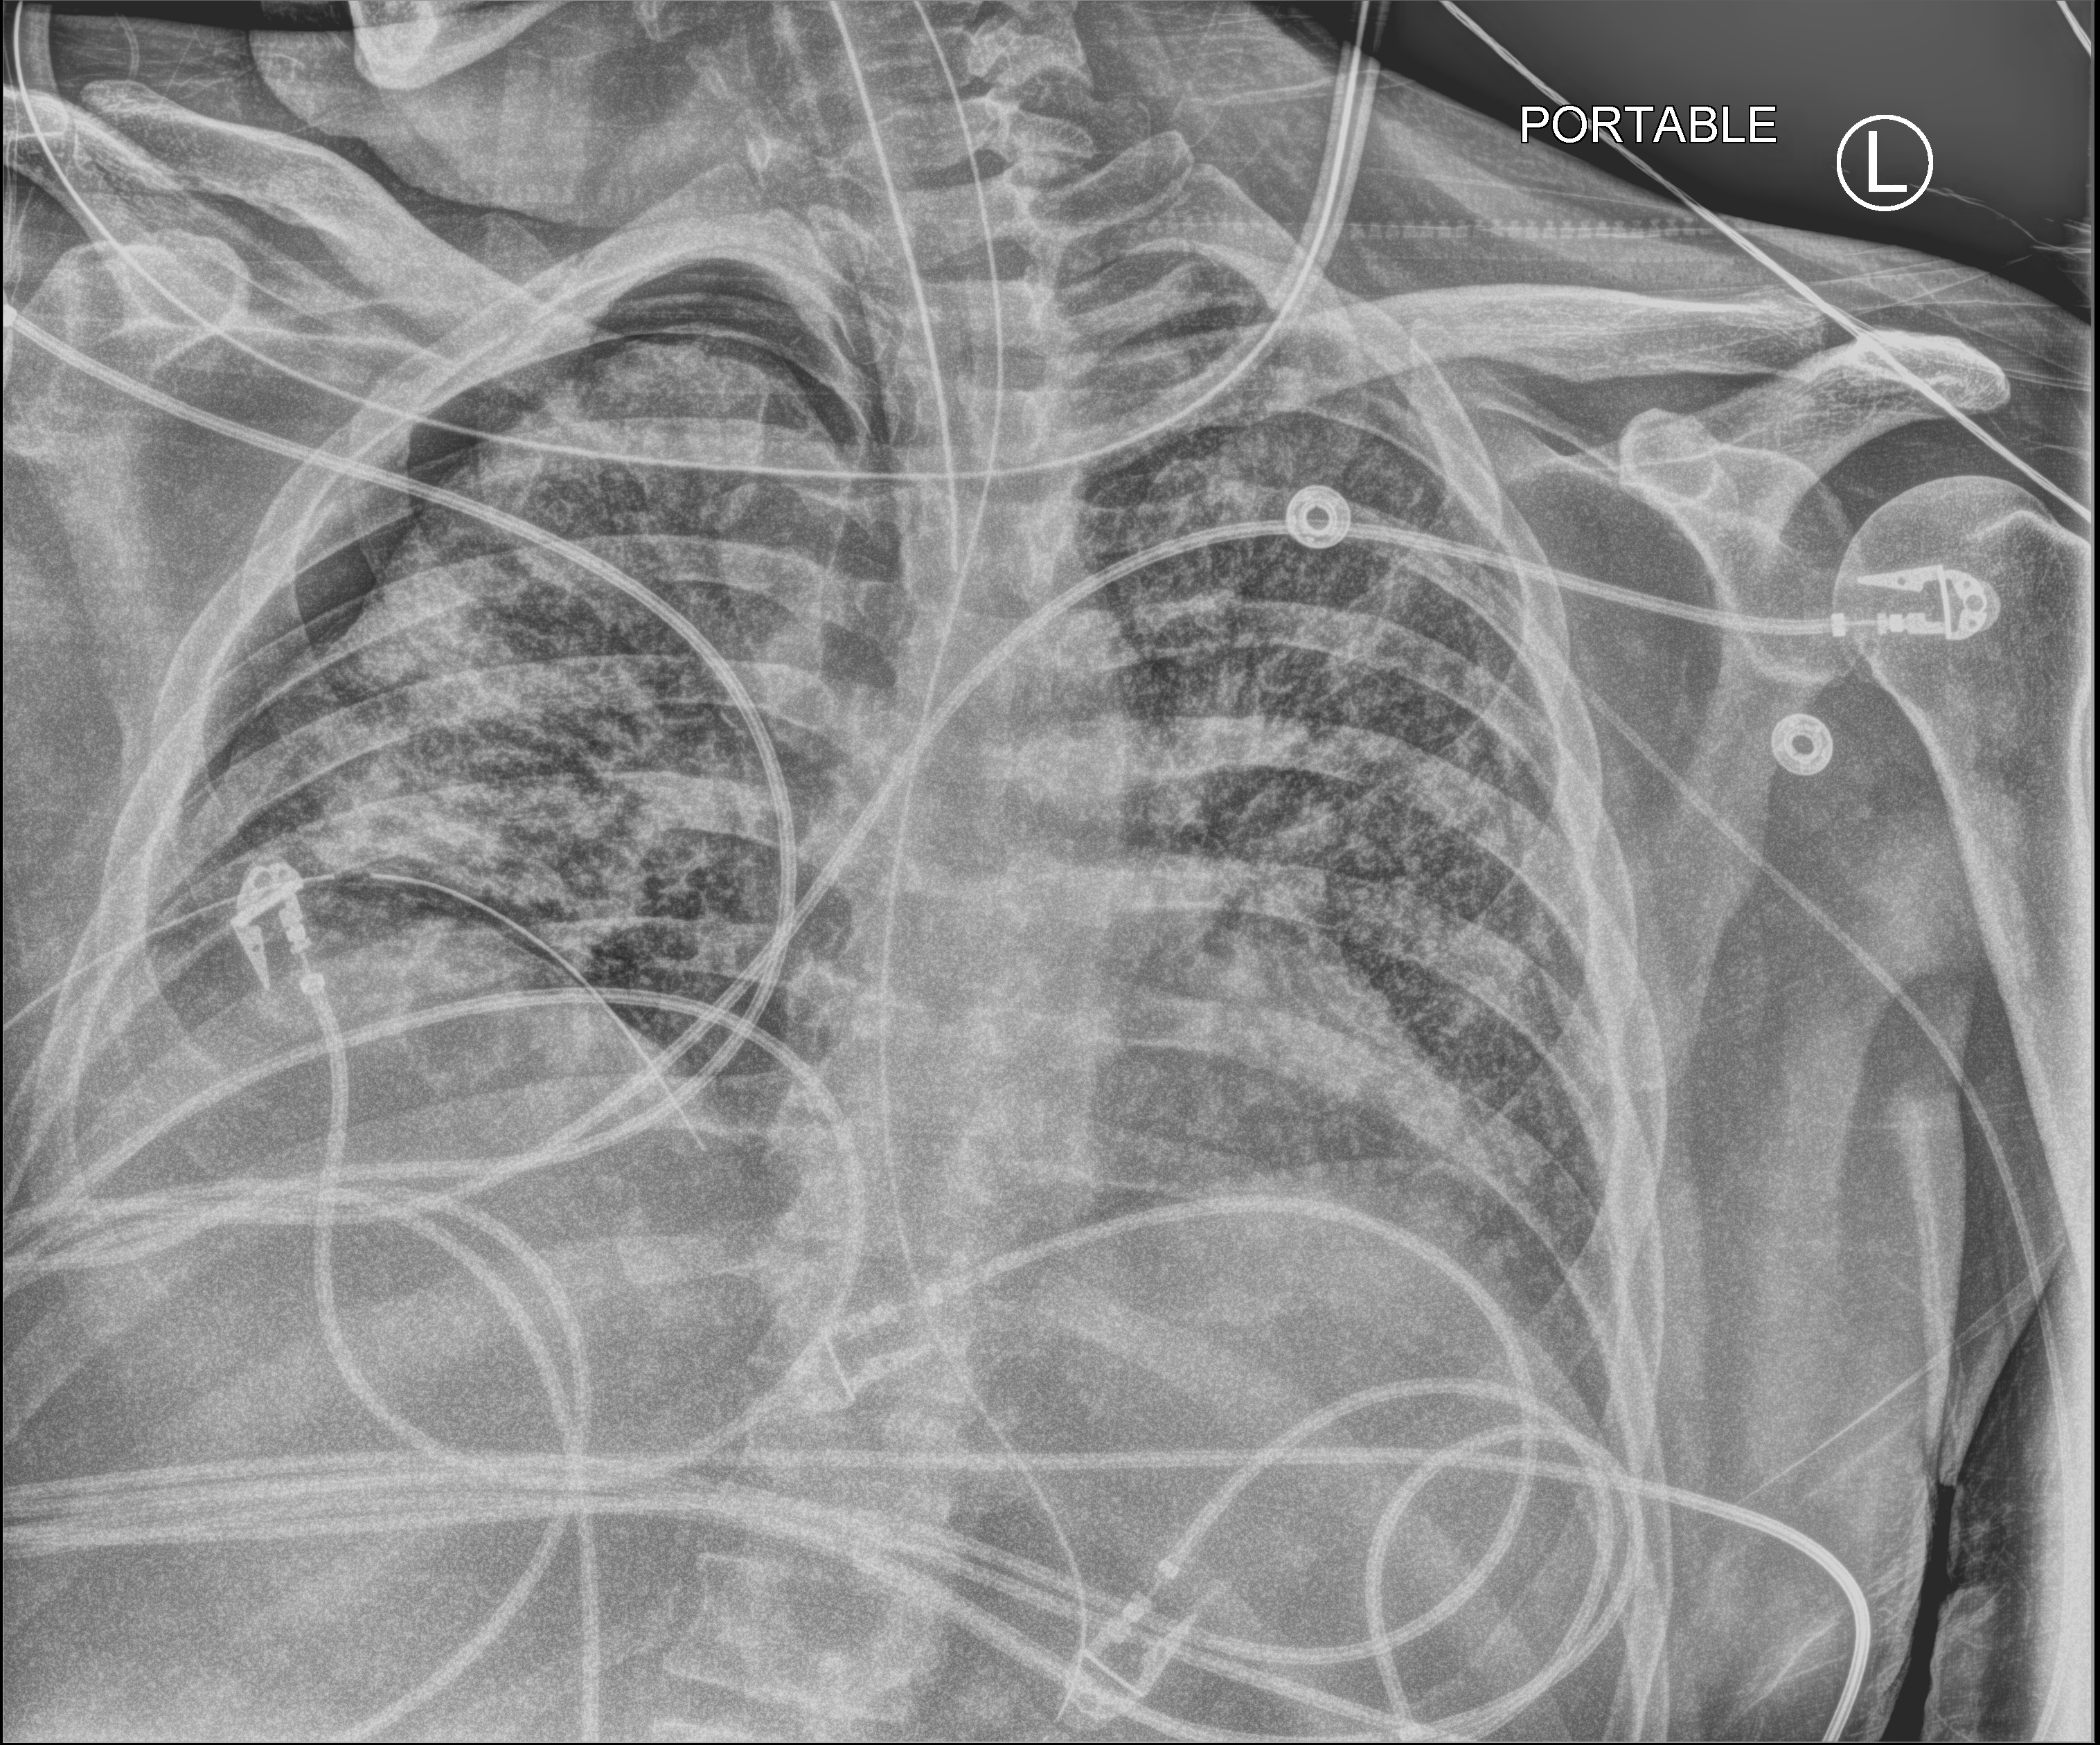
Portable chest radiograph, anteroposterior (AP) projection. Male patient hospitalised with COVID-19, age 18–59 years.
From the hospital-stay record, not from the radiograph (when in the stay this image was taken is not recorded): COPD (admission record): no; admitted to intensive care during this hospital stay: yes.